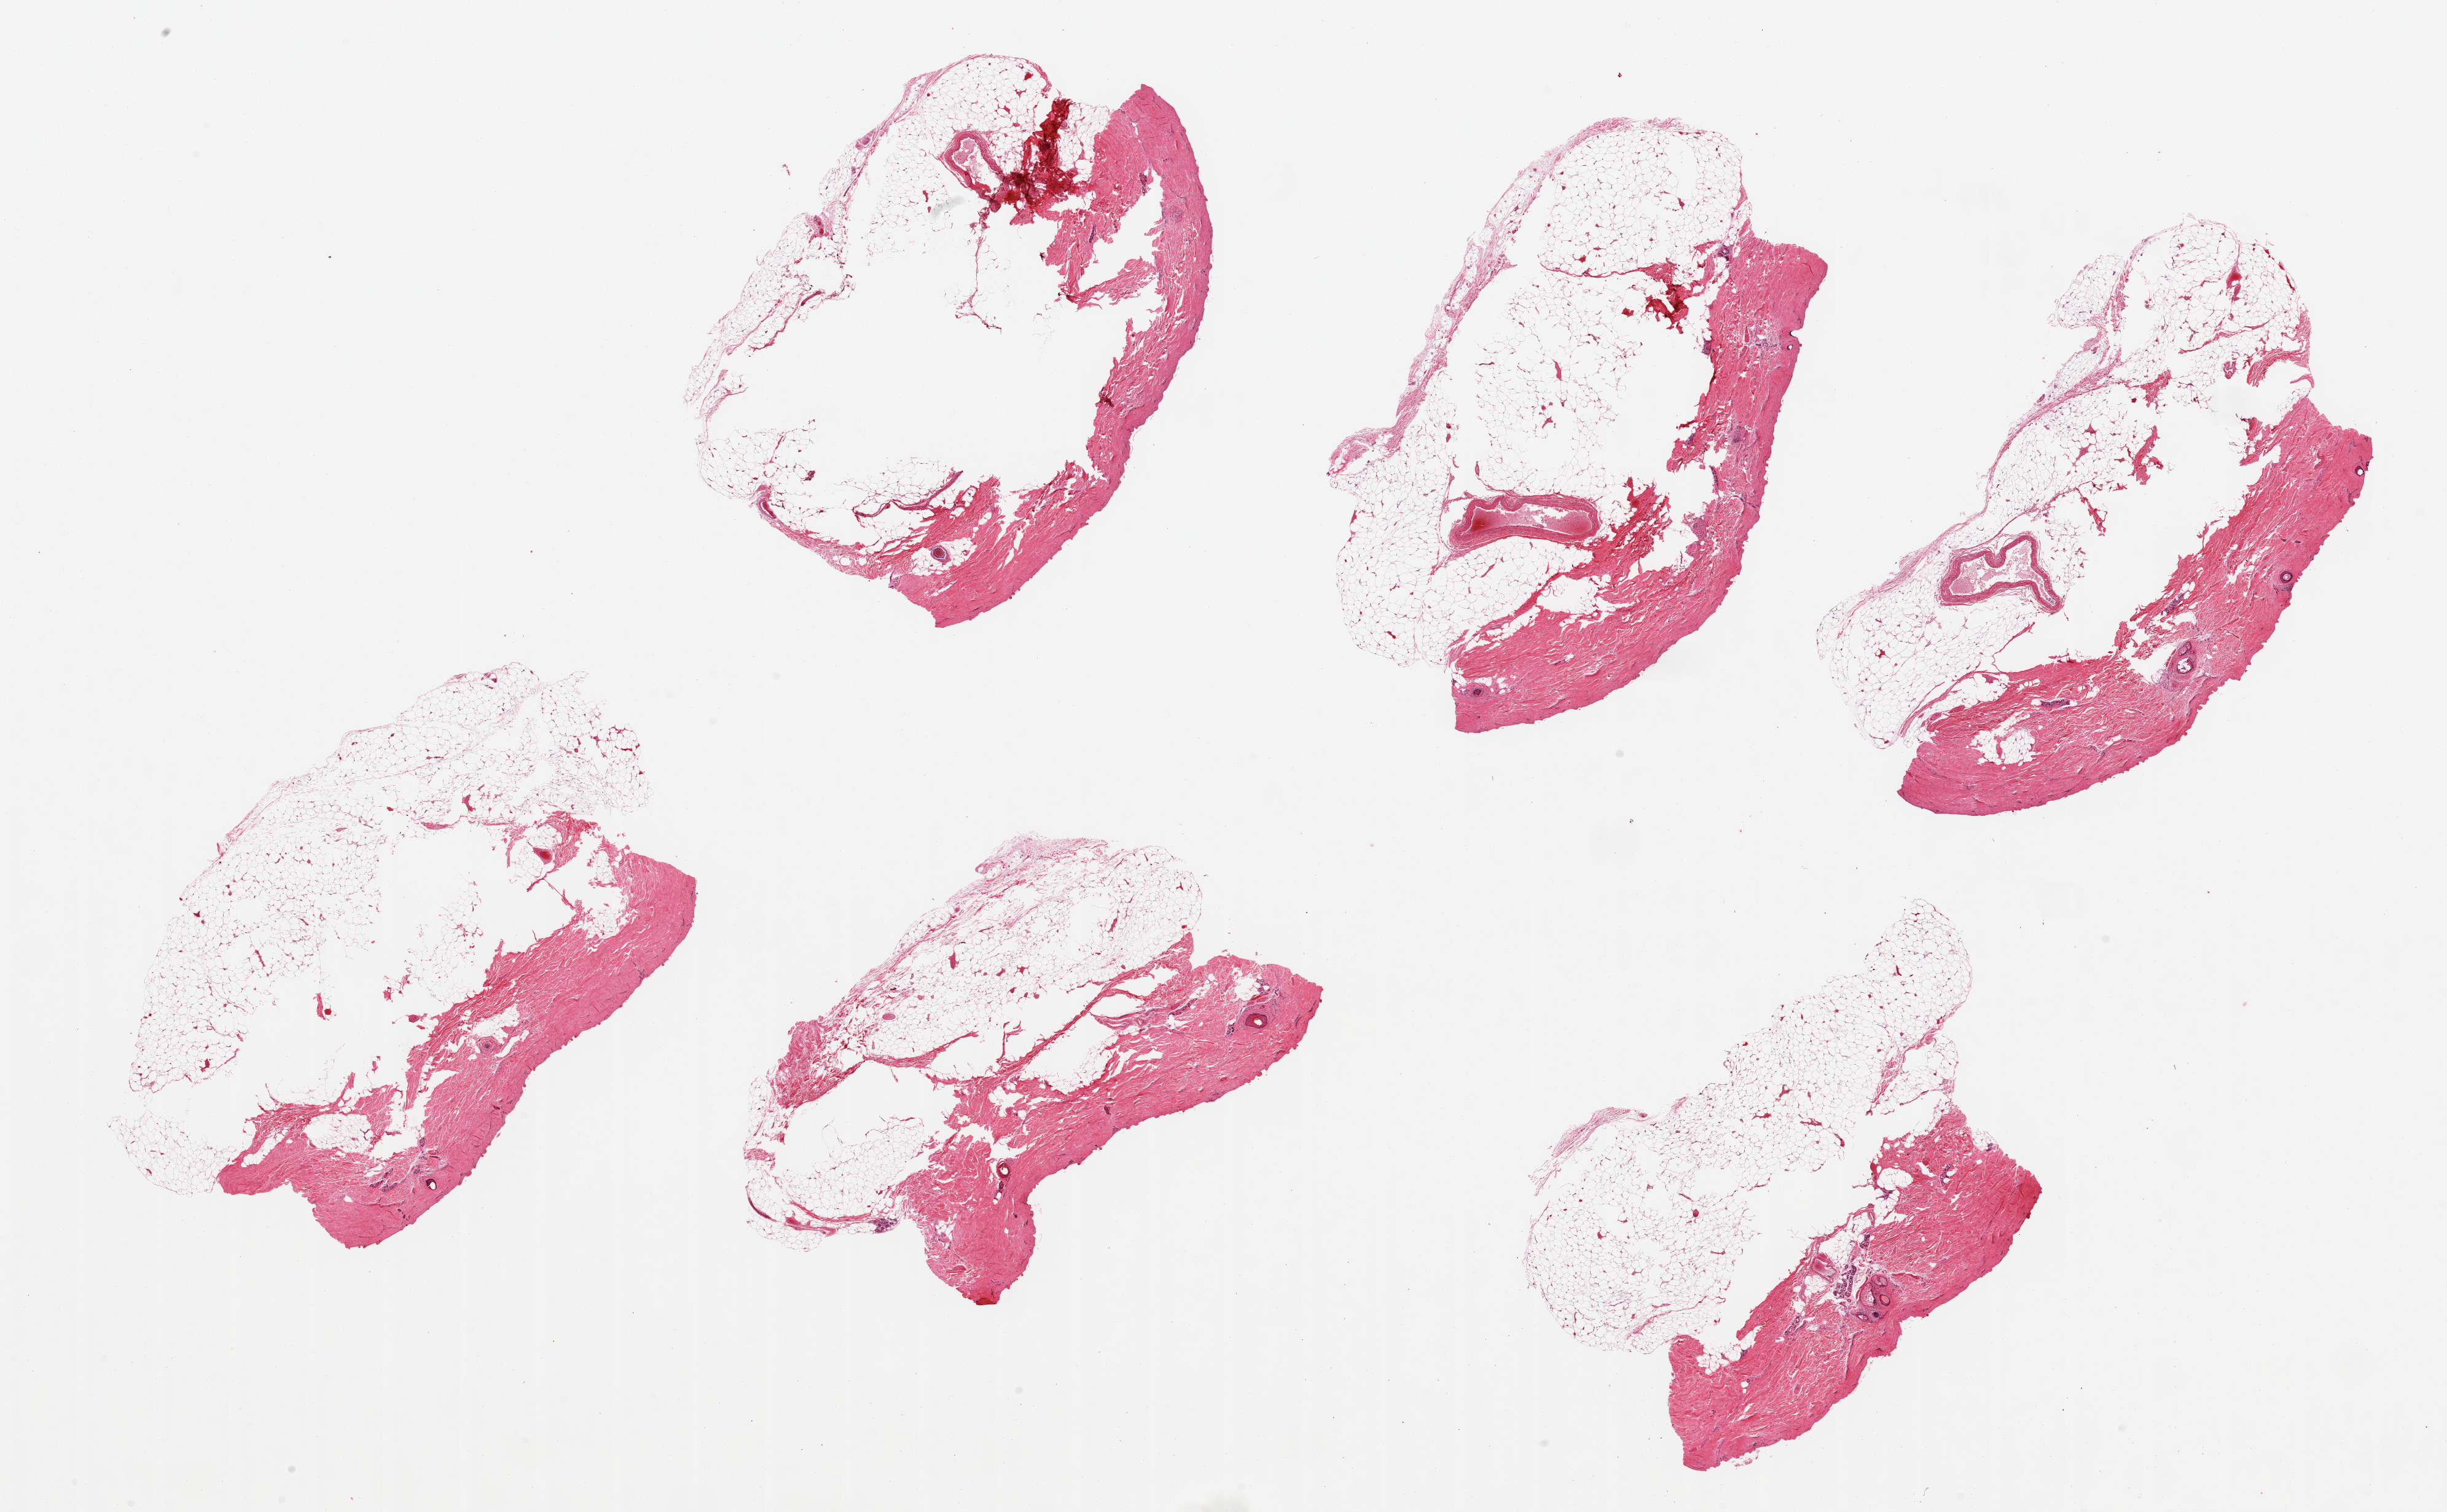
Whole-slide image, haematoxylin and eosin stain, brightfield, a low-resolution overview of the entire scanned area, about 31.5 x 19.5 mm. PAXgene-fixed, paraffin-embedded tissue. Target tissue: skin of lower leg. Tissue donor sample. Donor: male.
Review note (as recorded): 6 pieces up to 7.4x5 mm; excessive subcutaneous adipose tissue over 50% of specimens; epidermis completely sloughed.